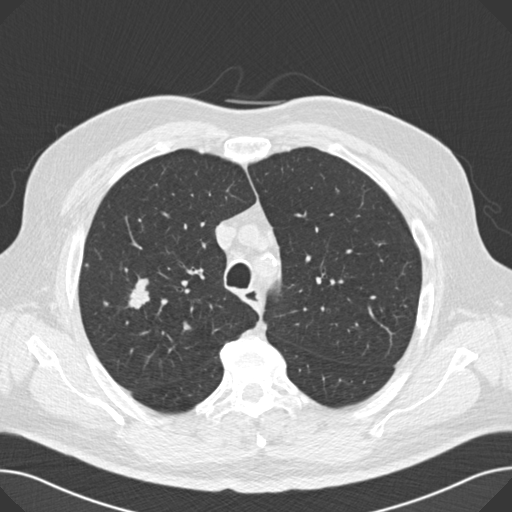
Low-dose screening chest CT, axial slice. Second annual screen. Lung window (W 1500 / L -600 HU). 2 mm slice thickness. Slice 45 of 166 in the series. Male, age 67 years at enrolment. Current smoker at enrolment.
Lesion marked by an expert reader, bounding box (x1, y1, x2, y2) in pixels: (122, 276, 160, 312). No non-calcified nodule or mass ≥4 mm was recorded by the screening reader at this exam. Later outcome: lung cancer diagnosed 194 days after this screen — small cell carcinoma, NOS, right middle lobe, stage IA (AJCC 6th edition), 20 mm at pathology.